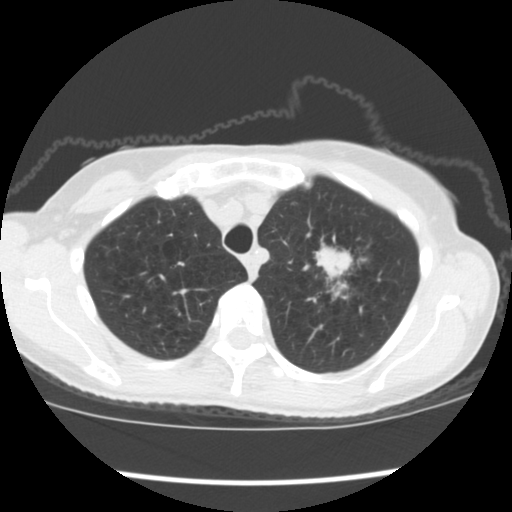
Chest CT (low-dose screening protocol), one axial image; baseline screening round; lung window (W 1500 / L -600 HU); 2.5 mm slice thickness; standard (soft-tissue) reconstruction kernel (STANDARD). Female participant, aged 67 years at enrolment. Former smoker at enrolment.
Lesion marked by an expert reader, box from (x=303, y=236) to (x=375, y=310) px. Reader record for this screening exam (exam-level; its link to the box is not recorded): non-calcified nodule or mass ≥4 mm, left upper lobe, 34 × 32 mm, spiculated (stellate) margins, soft tissue attenuation, pre-existing on the prior screen: no. Participant outcome: lung cancer diagnosed 17 days after this screen — small cell carcinoma, NOS, left upper lobe, stage IIIA (AJCC 6th edition), 40 mm at pathology.